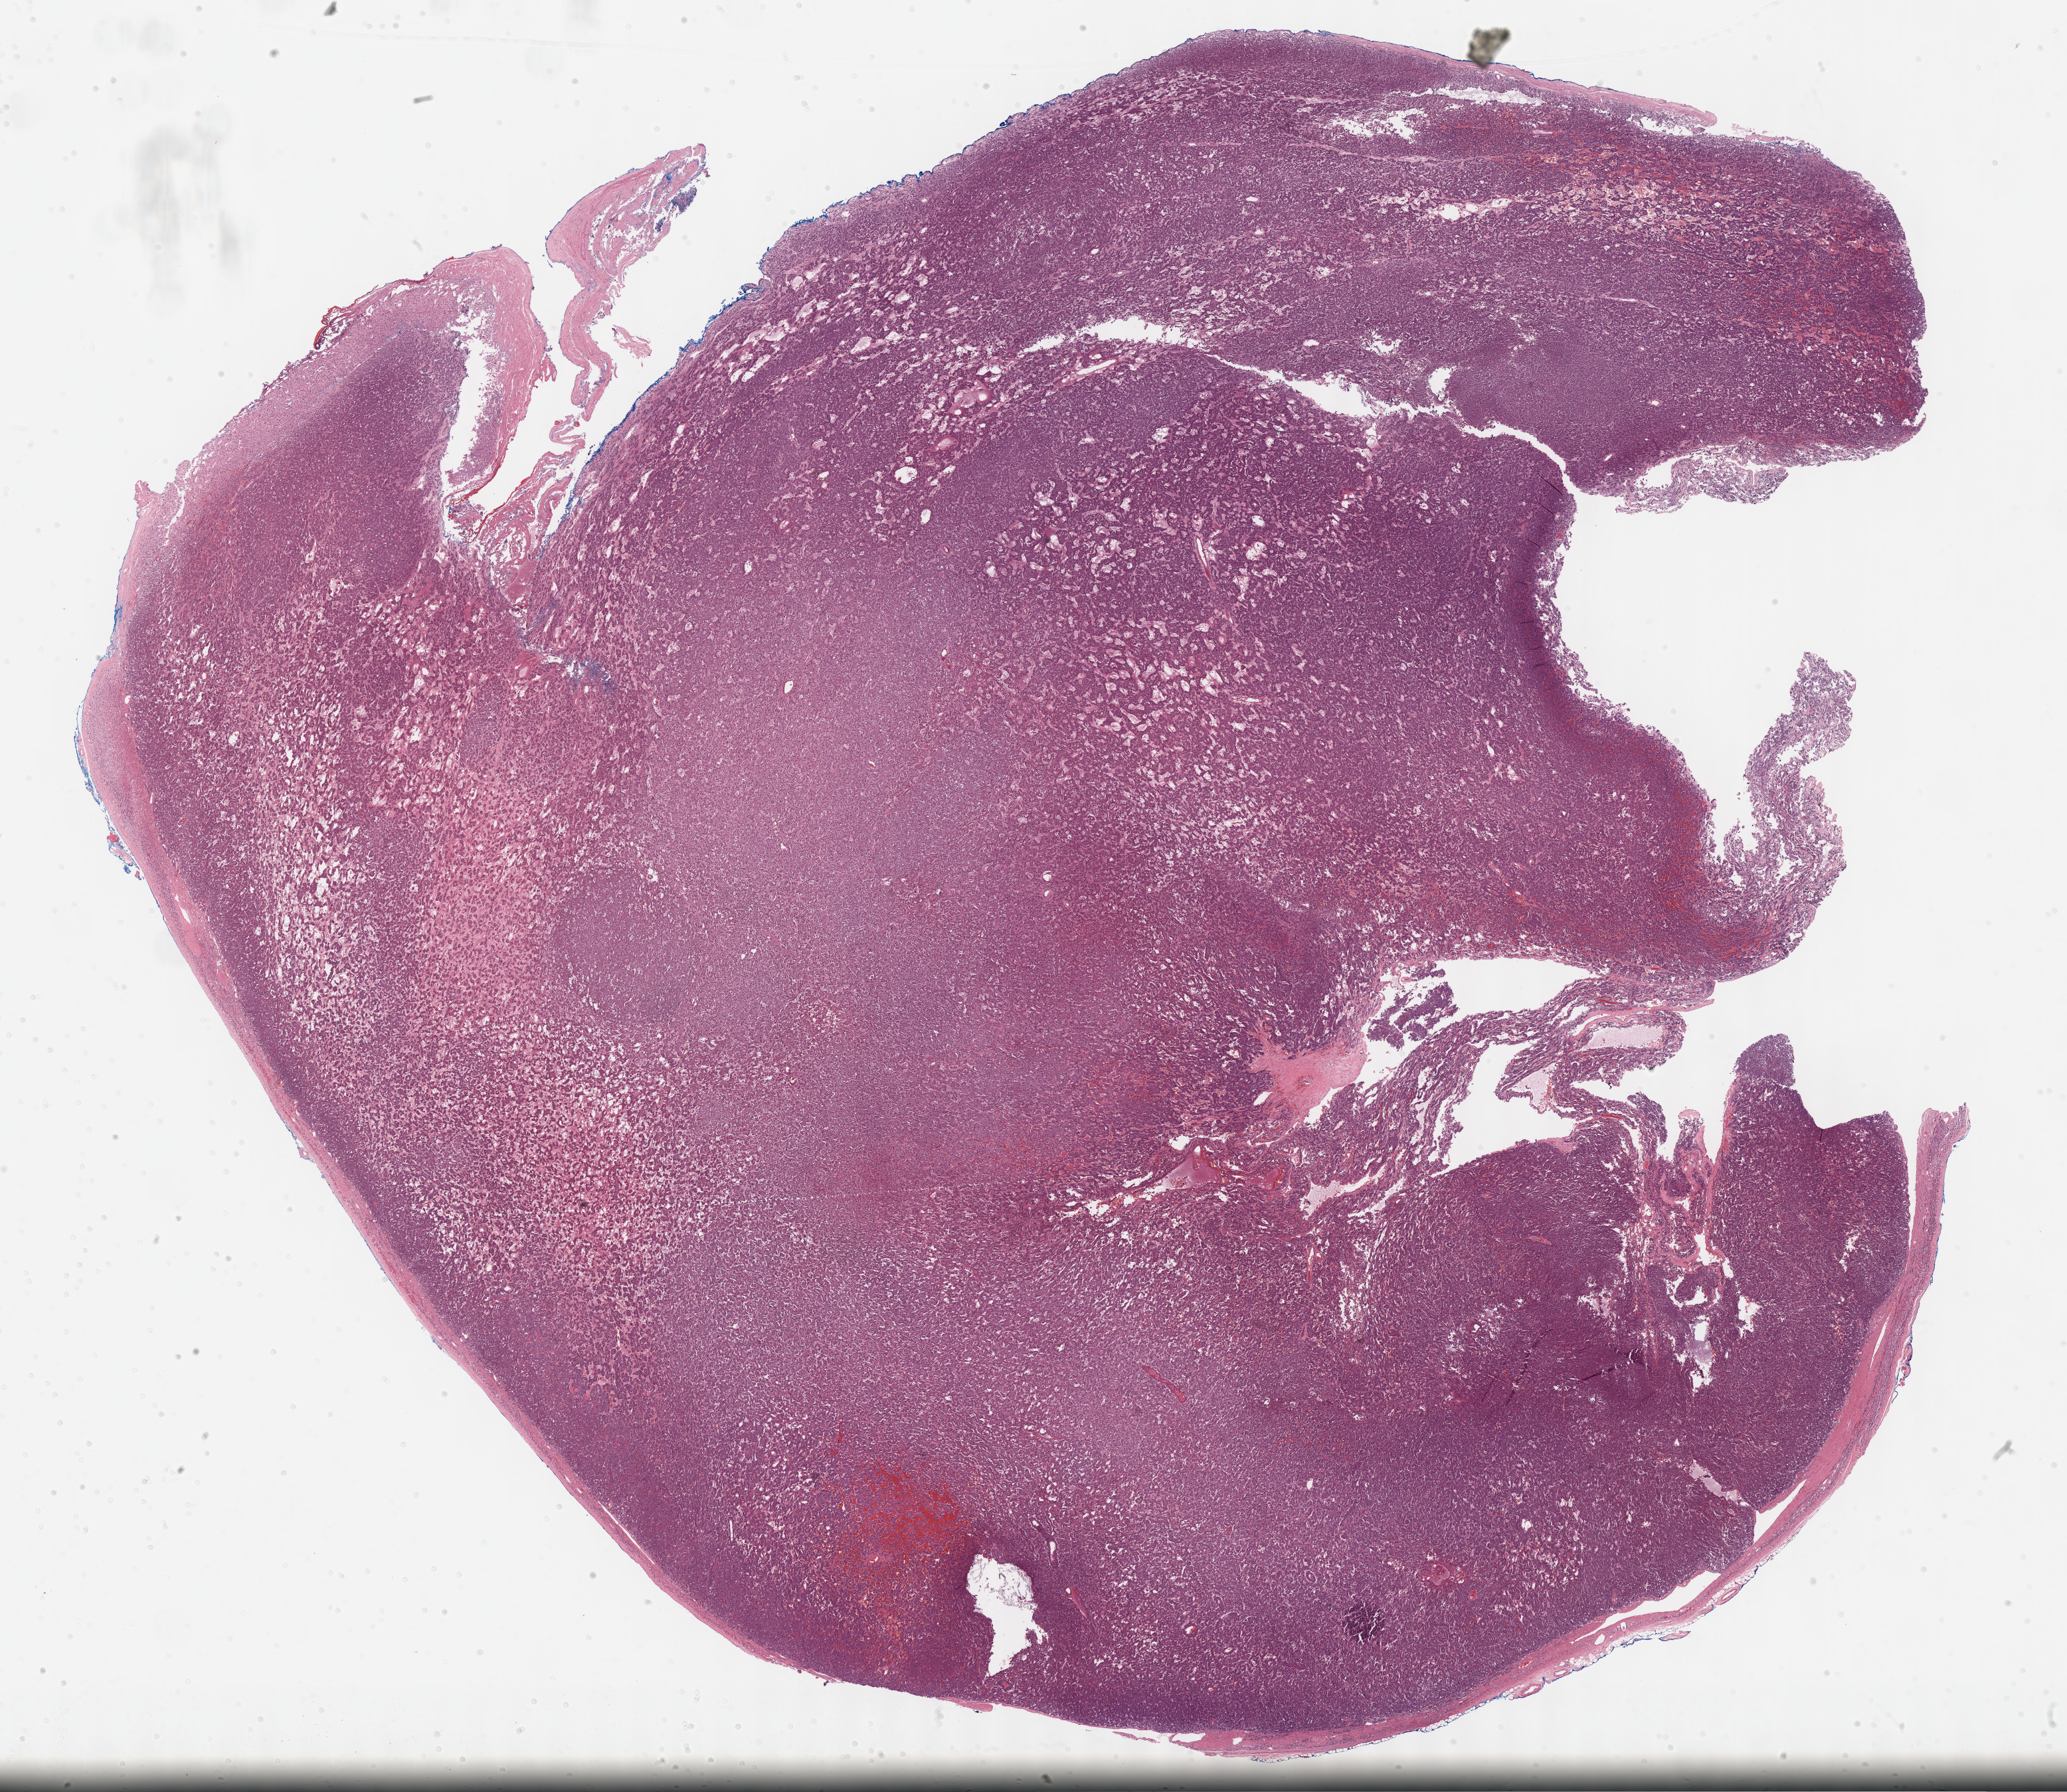
Whole-slide histology image, H&E, a low-resolution overview of the entire scanned area, about 25.2 x 21.8 mm, FFPE section, primary tumour sample from the adrenal gland. Female, age 43 years at initial diagnosis.
Histologic diagnosis: Pheochromocytoma, NOS.